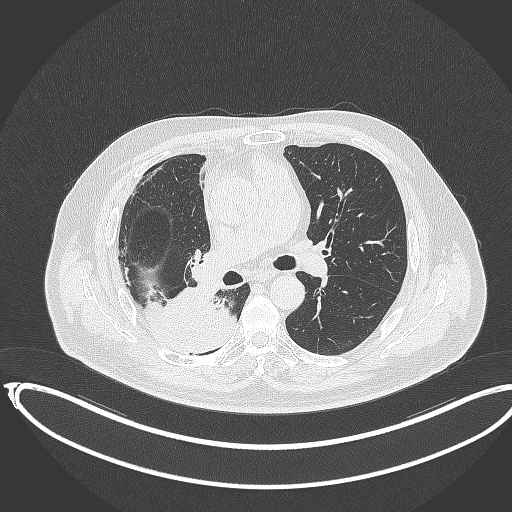
Chest CT, one axial slice; position 203 of 403 along the scan axis; 120 kVp; lung window (W 1500 / L -600 HU); 1 mm slice thickness; 512 × 512 image matrix. Male patient, age 68 years. From the clinical record (not read from this slice): clinical TNM (as recorded): T2a N0 M0.
Structures marked on this image (bounding box drawn by a radiologist):
- lung tumour (recorded histology: adenocarcinoma): box from (x=143, y=293) to (x=238, y=351) px